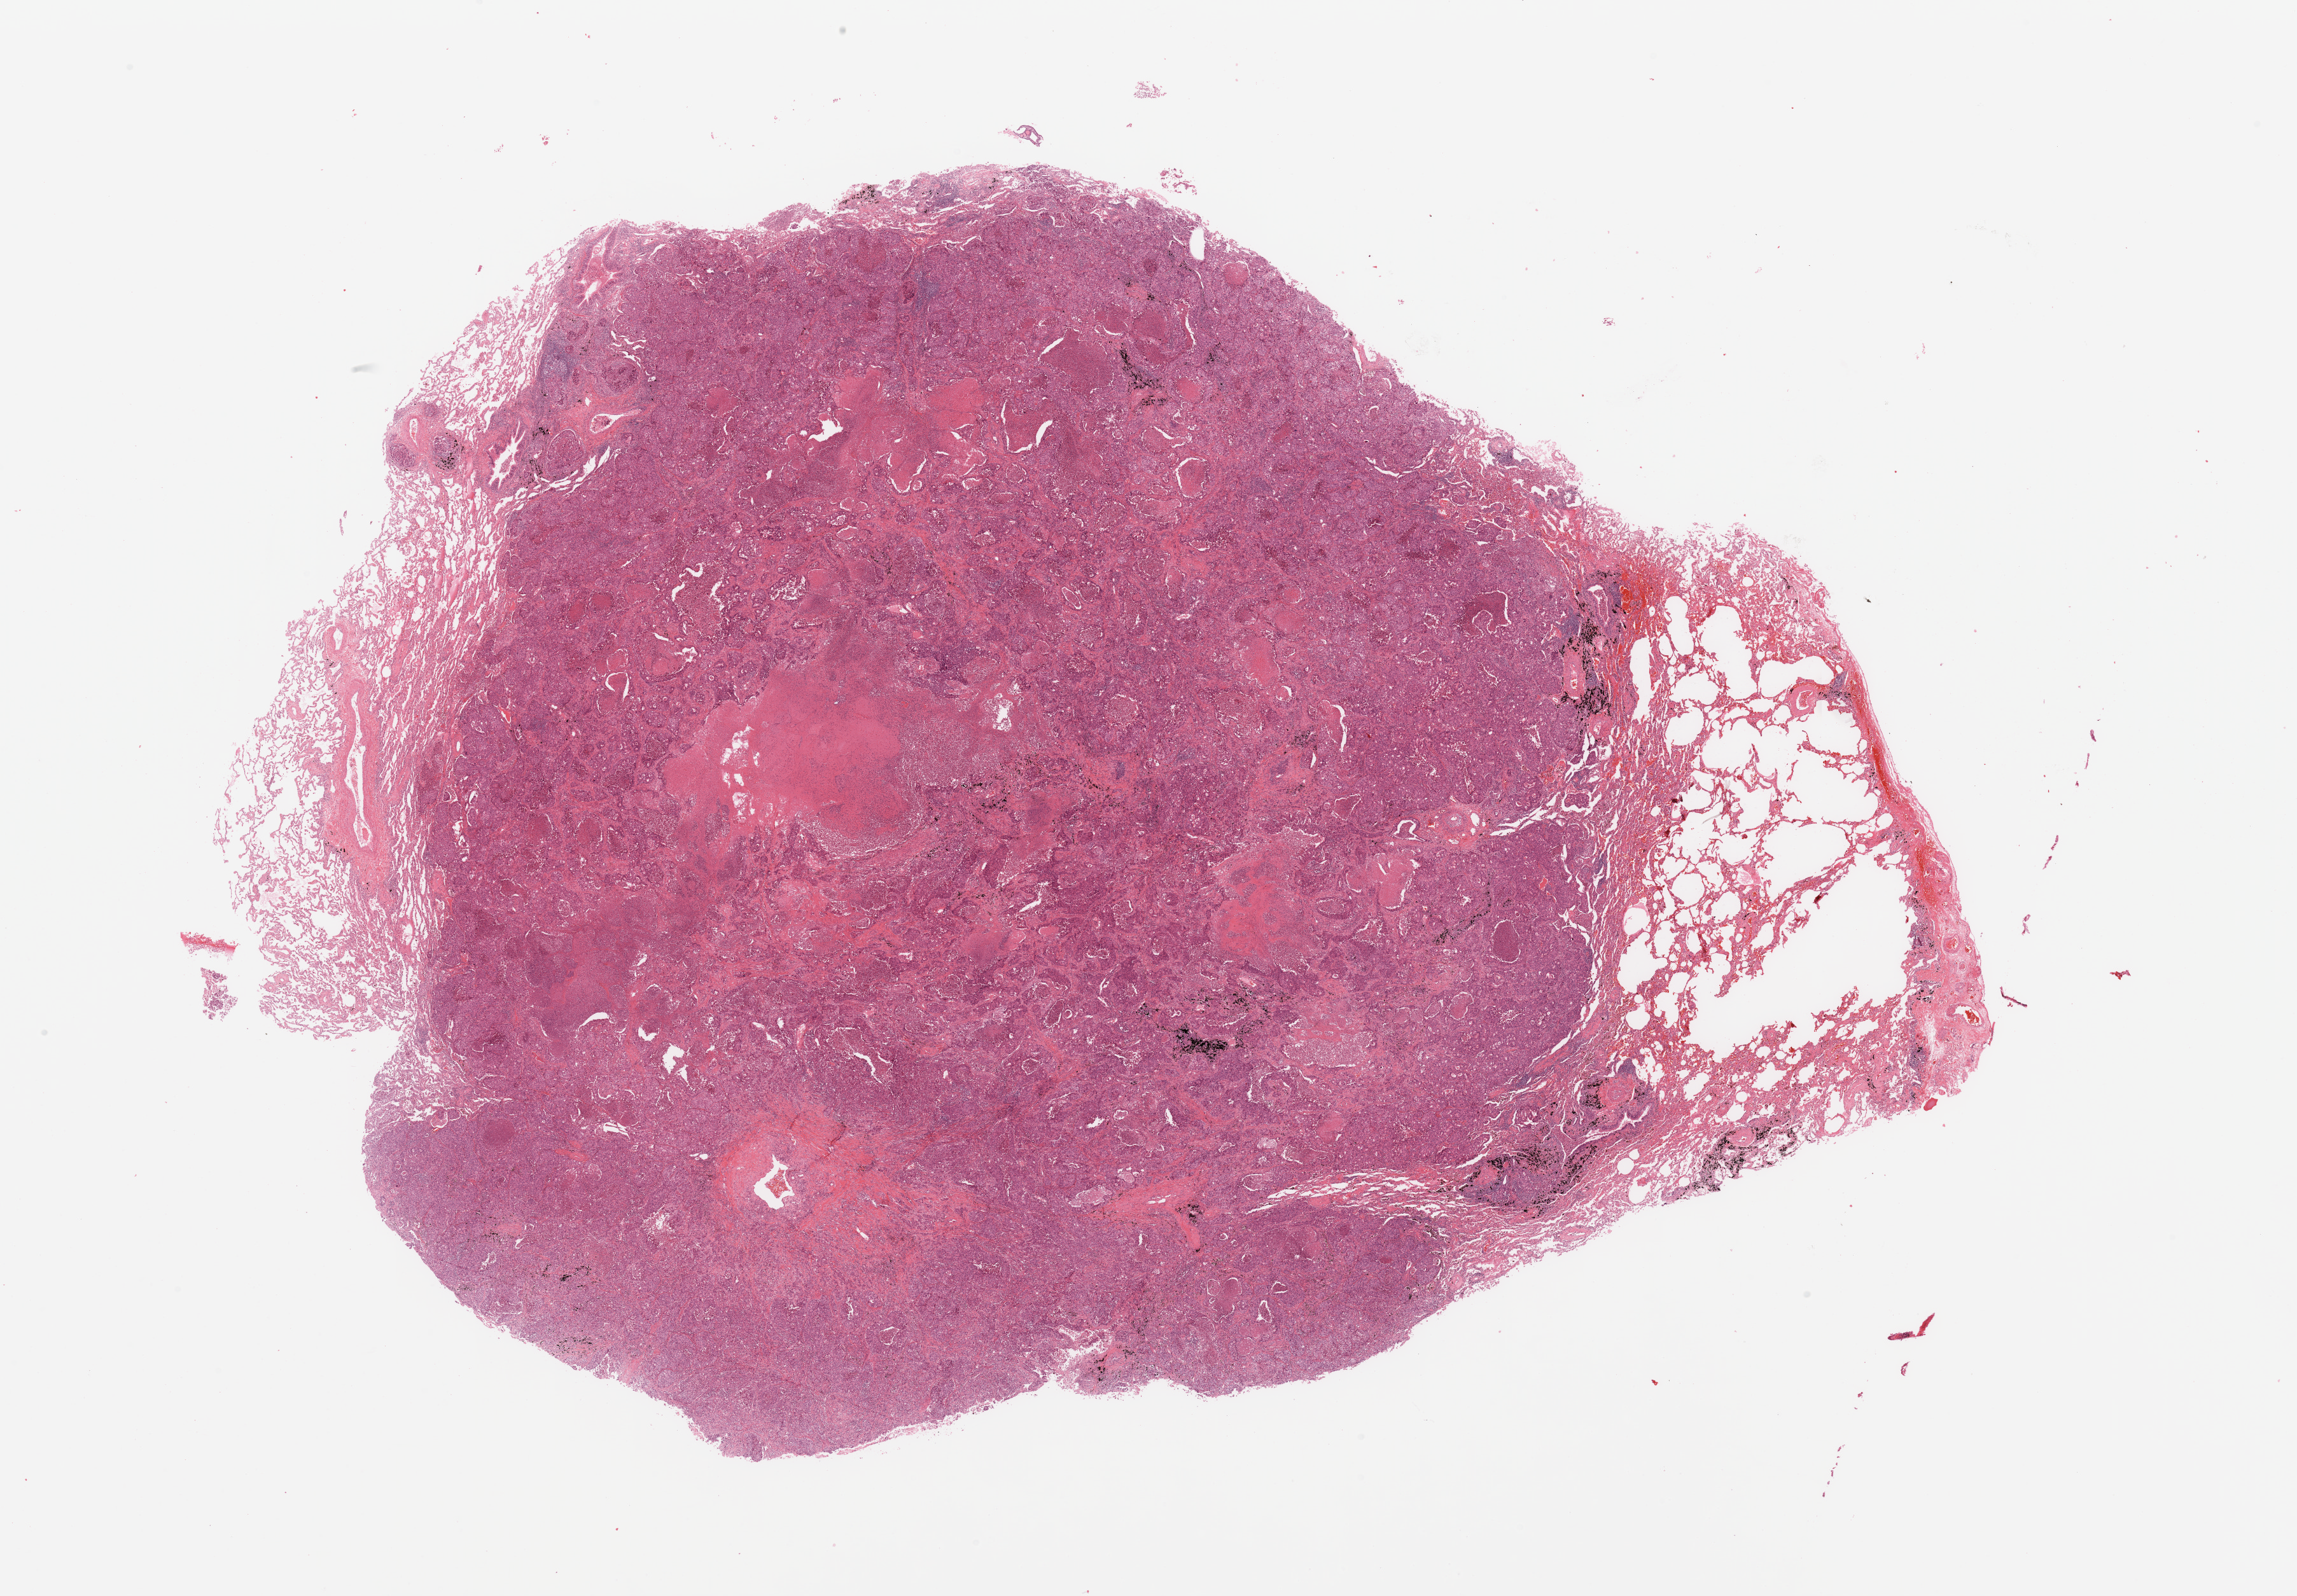
Whole-slide histology image, H&E, low-resolution overview of the scanned area, about 28.5 x 19.8 mm (acquisition: 20x scan), lung, tumour tissue. 64-year-old male patient.
Patient diagnosis (cohort enrolment): squamous cell carcinoma (lung).